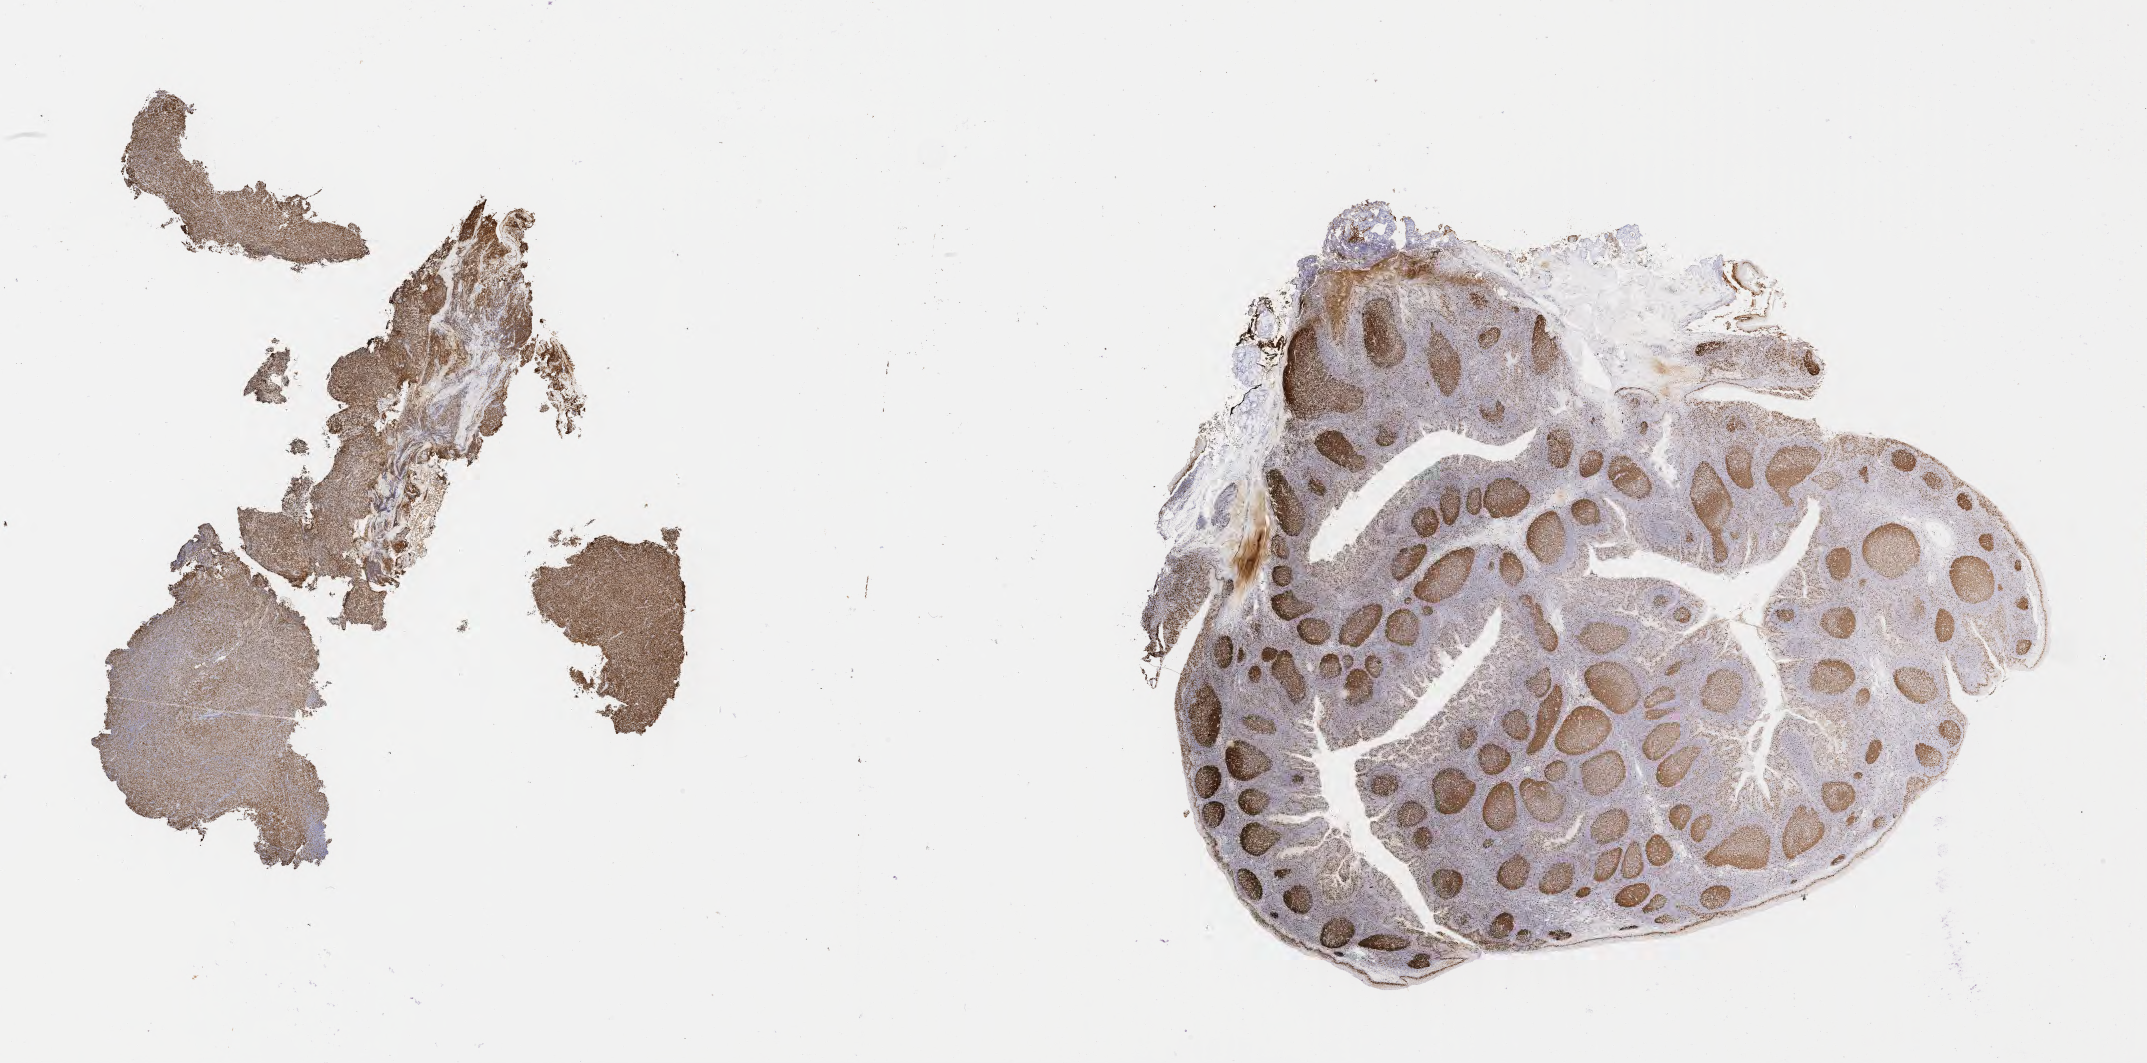
IHC for Ki-67, whole-slide image, low-resolution overview of the scanned area, about 34.7 x 17.2 mm; tumor tissue; site: liver. Patient female; age 36 years.
Histologic diagnosis: Diffuse large B-cell lymphoma, NOS.